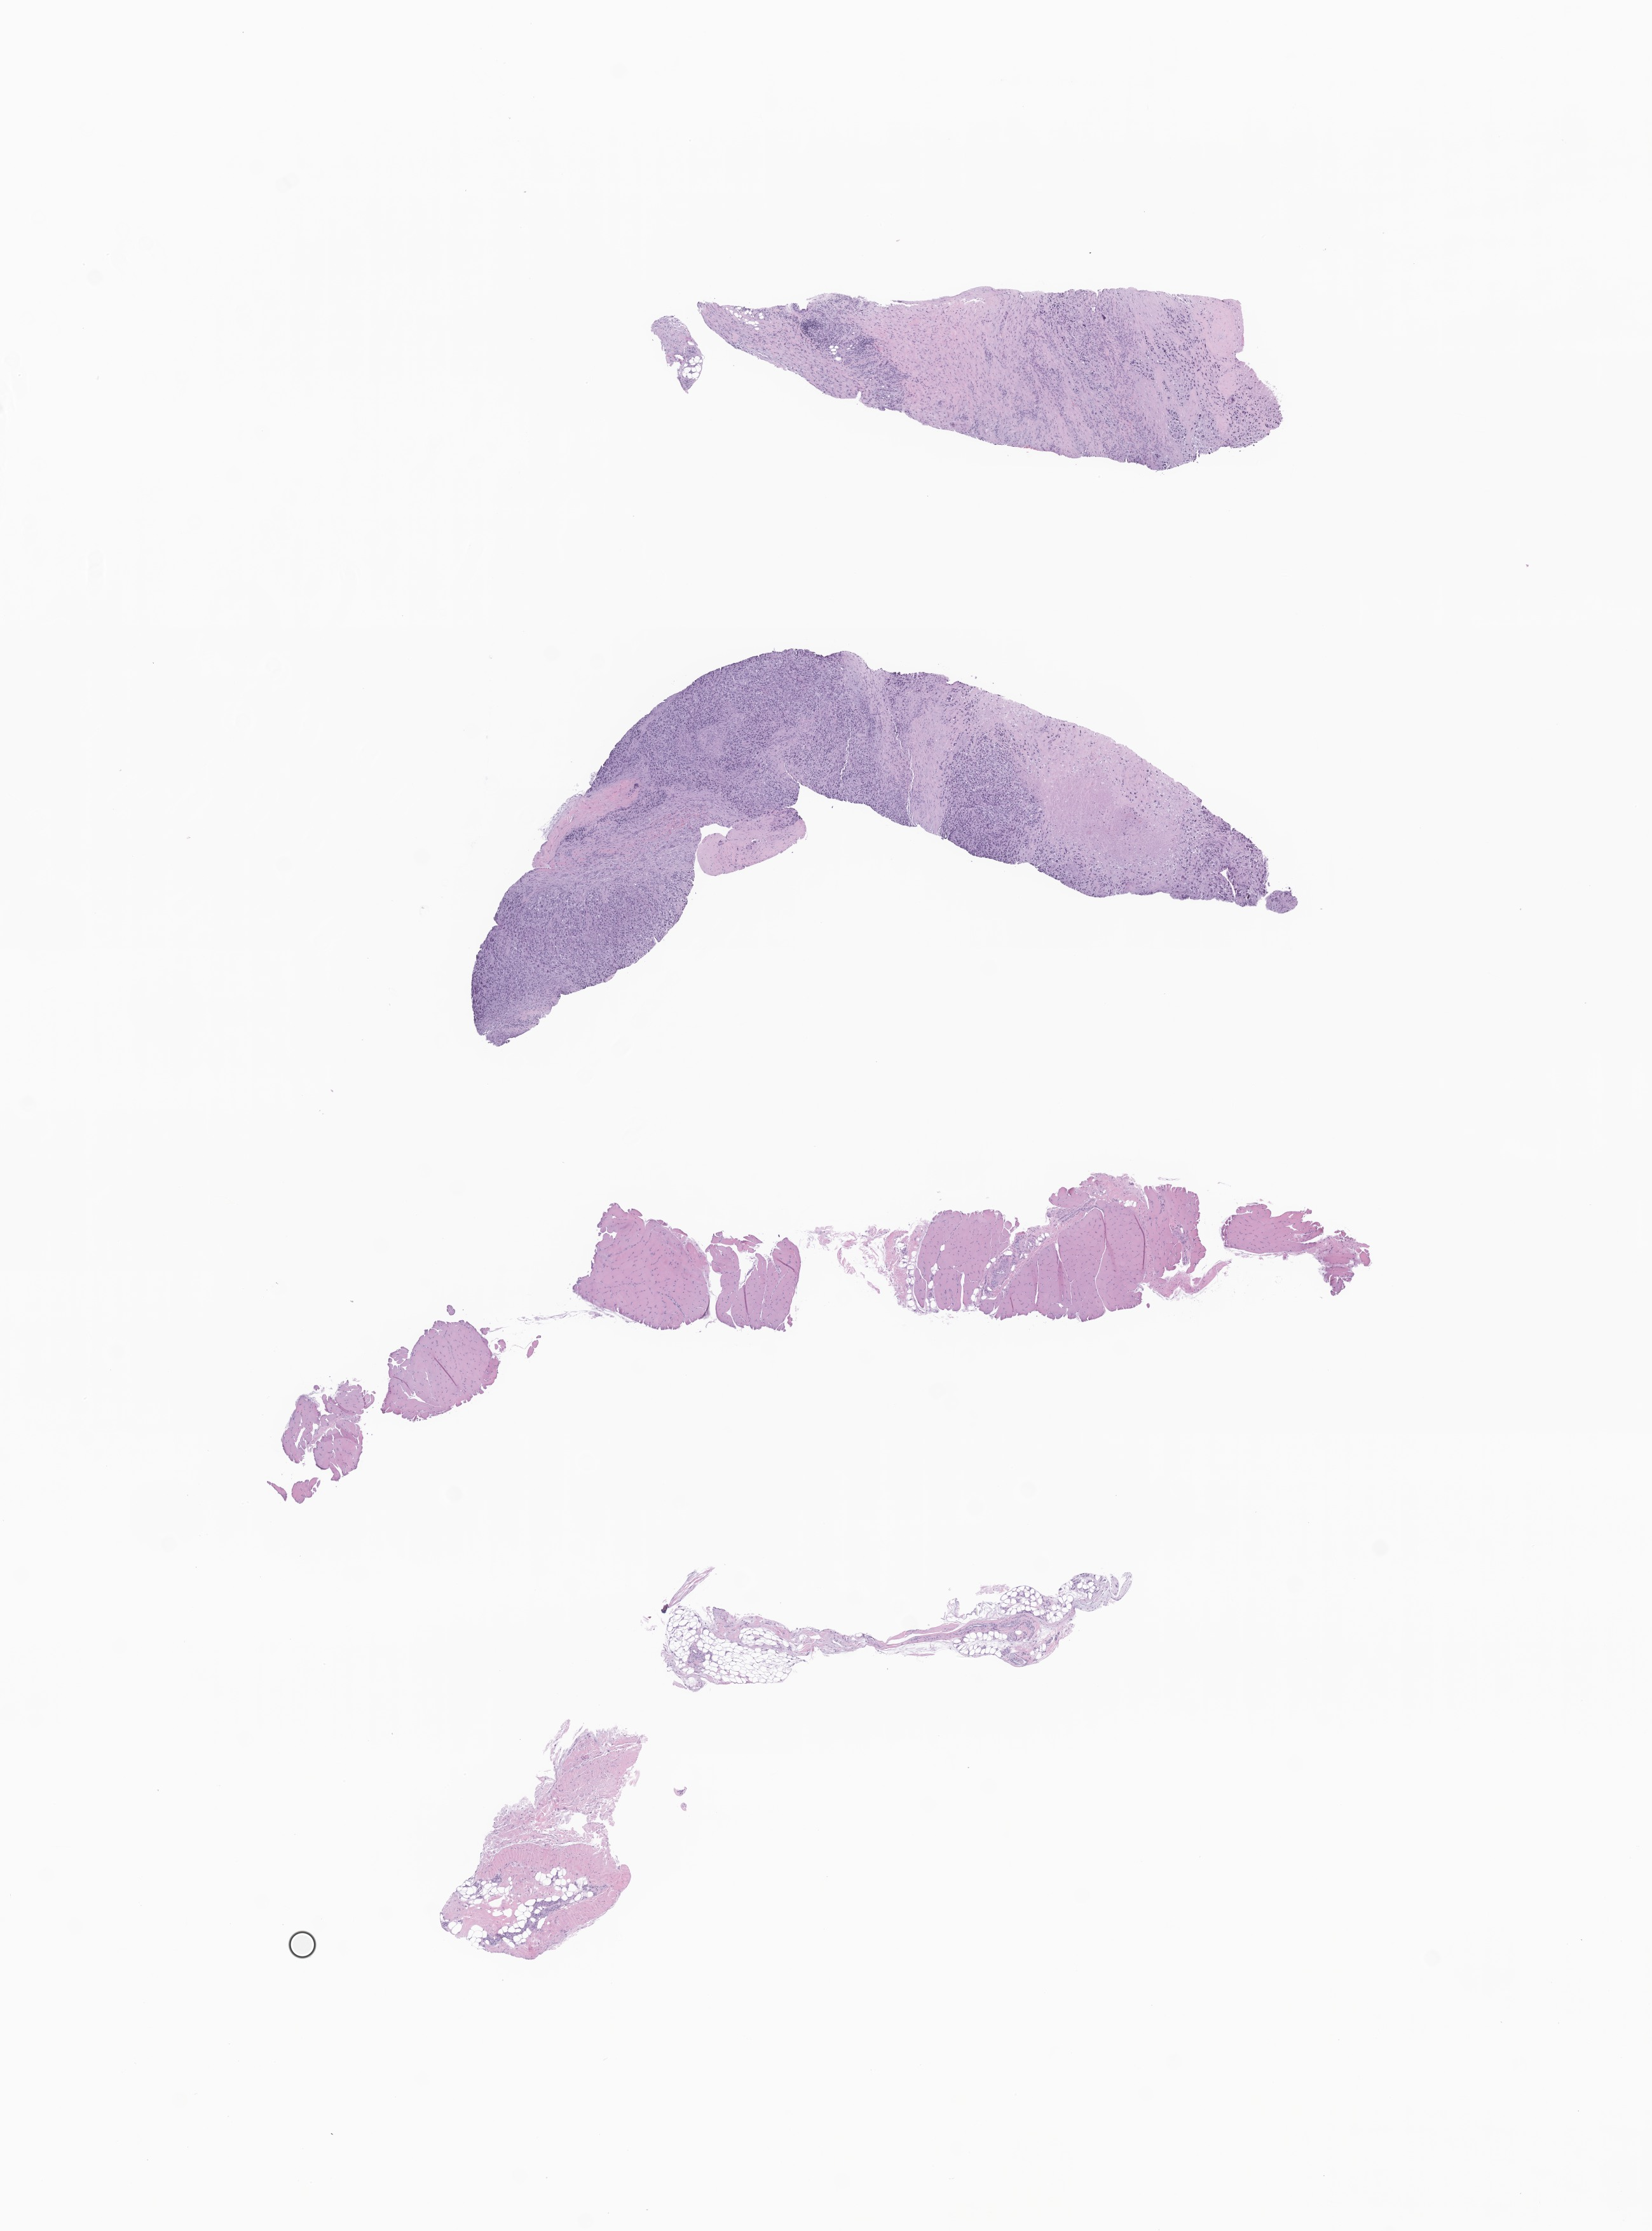
Whole-slide image, H&E stain of tumor tissue from the soft tissue of lower extremity, whole scanned area (about 11.0 x 14.8 mm) shown as a low-resolution overview; FFPE section. Patient male; age 58 months (4 years 10 months).
Diagnosis: Rhabdomyosarcoma, NOS.